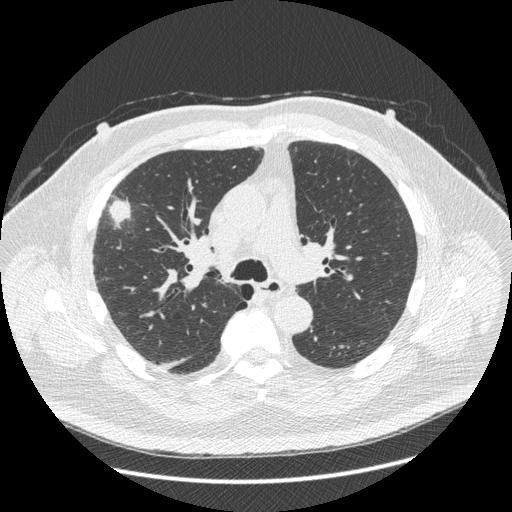
Low-dose screening chest CT, one axial slice. Position 274 of 426 along the scan axis. Reconstruction kernel STANDARD. 120 kVp. Lung window (W 1500 / L -600 HU). 512 × 512 image matrix, field of view 400 × 400 mm.
Structures marked on this image (expert manual segmentation):
- lesion 1 (tumor, upper lobe of right lung): box from (x=109, y=201) to (x=130, y=224) px